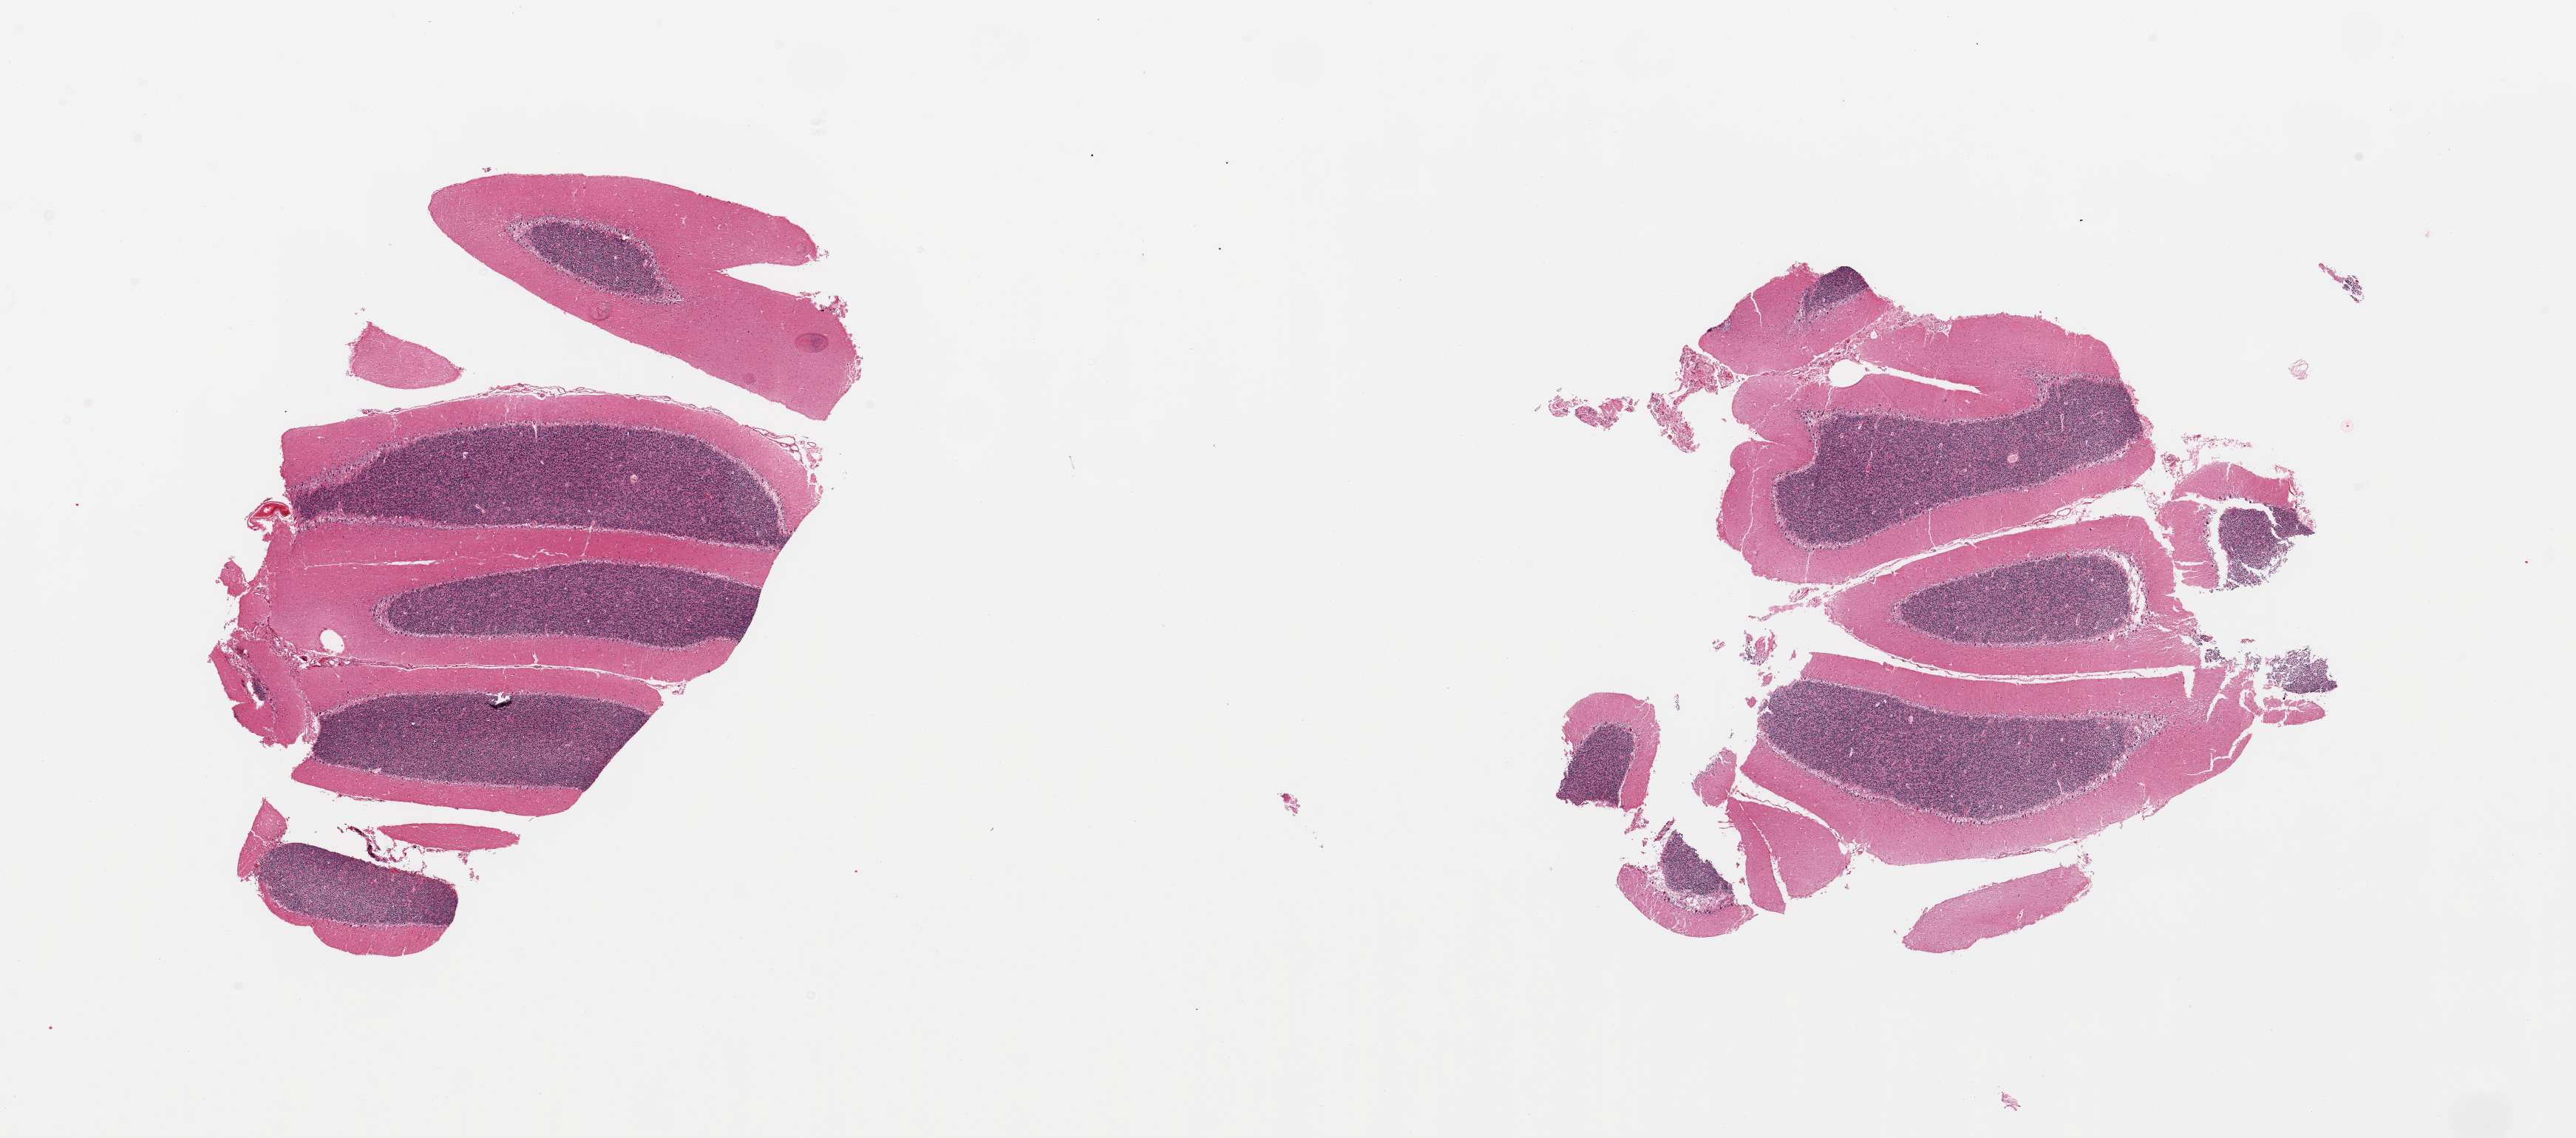
Whole-slide image, H&E stain, whole scanned area (about 27.6 x 12.2 mm) shown as a low-resolution overview. PAXgene-fixed paraffin-embedded (PFPE) section. Target tissue: cerebellum. Tissue donor sample.
Reviewer comment on this tissue sample: 2 pieces.